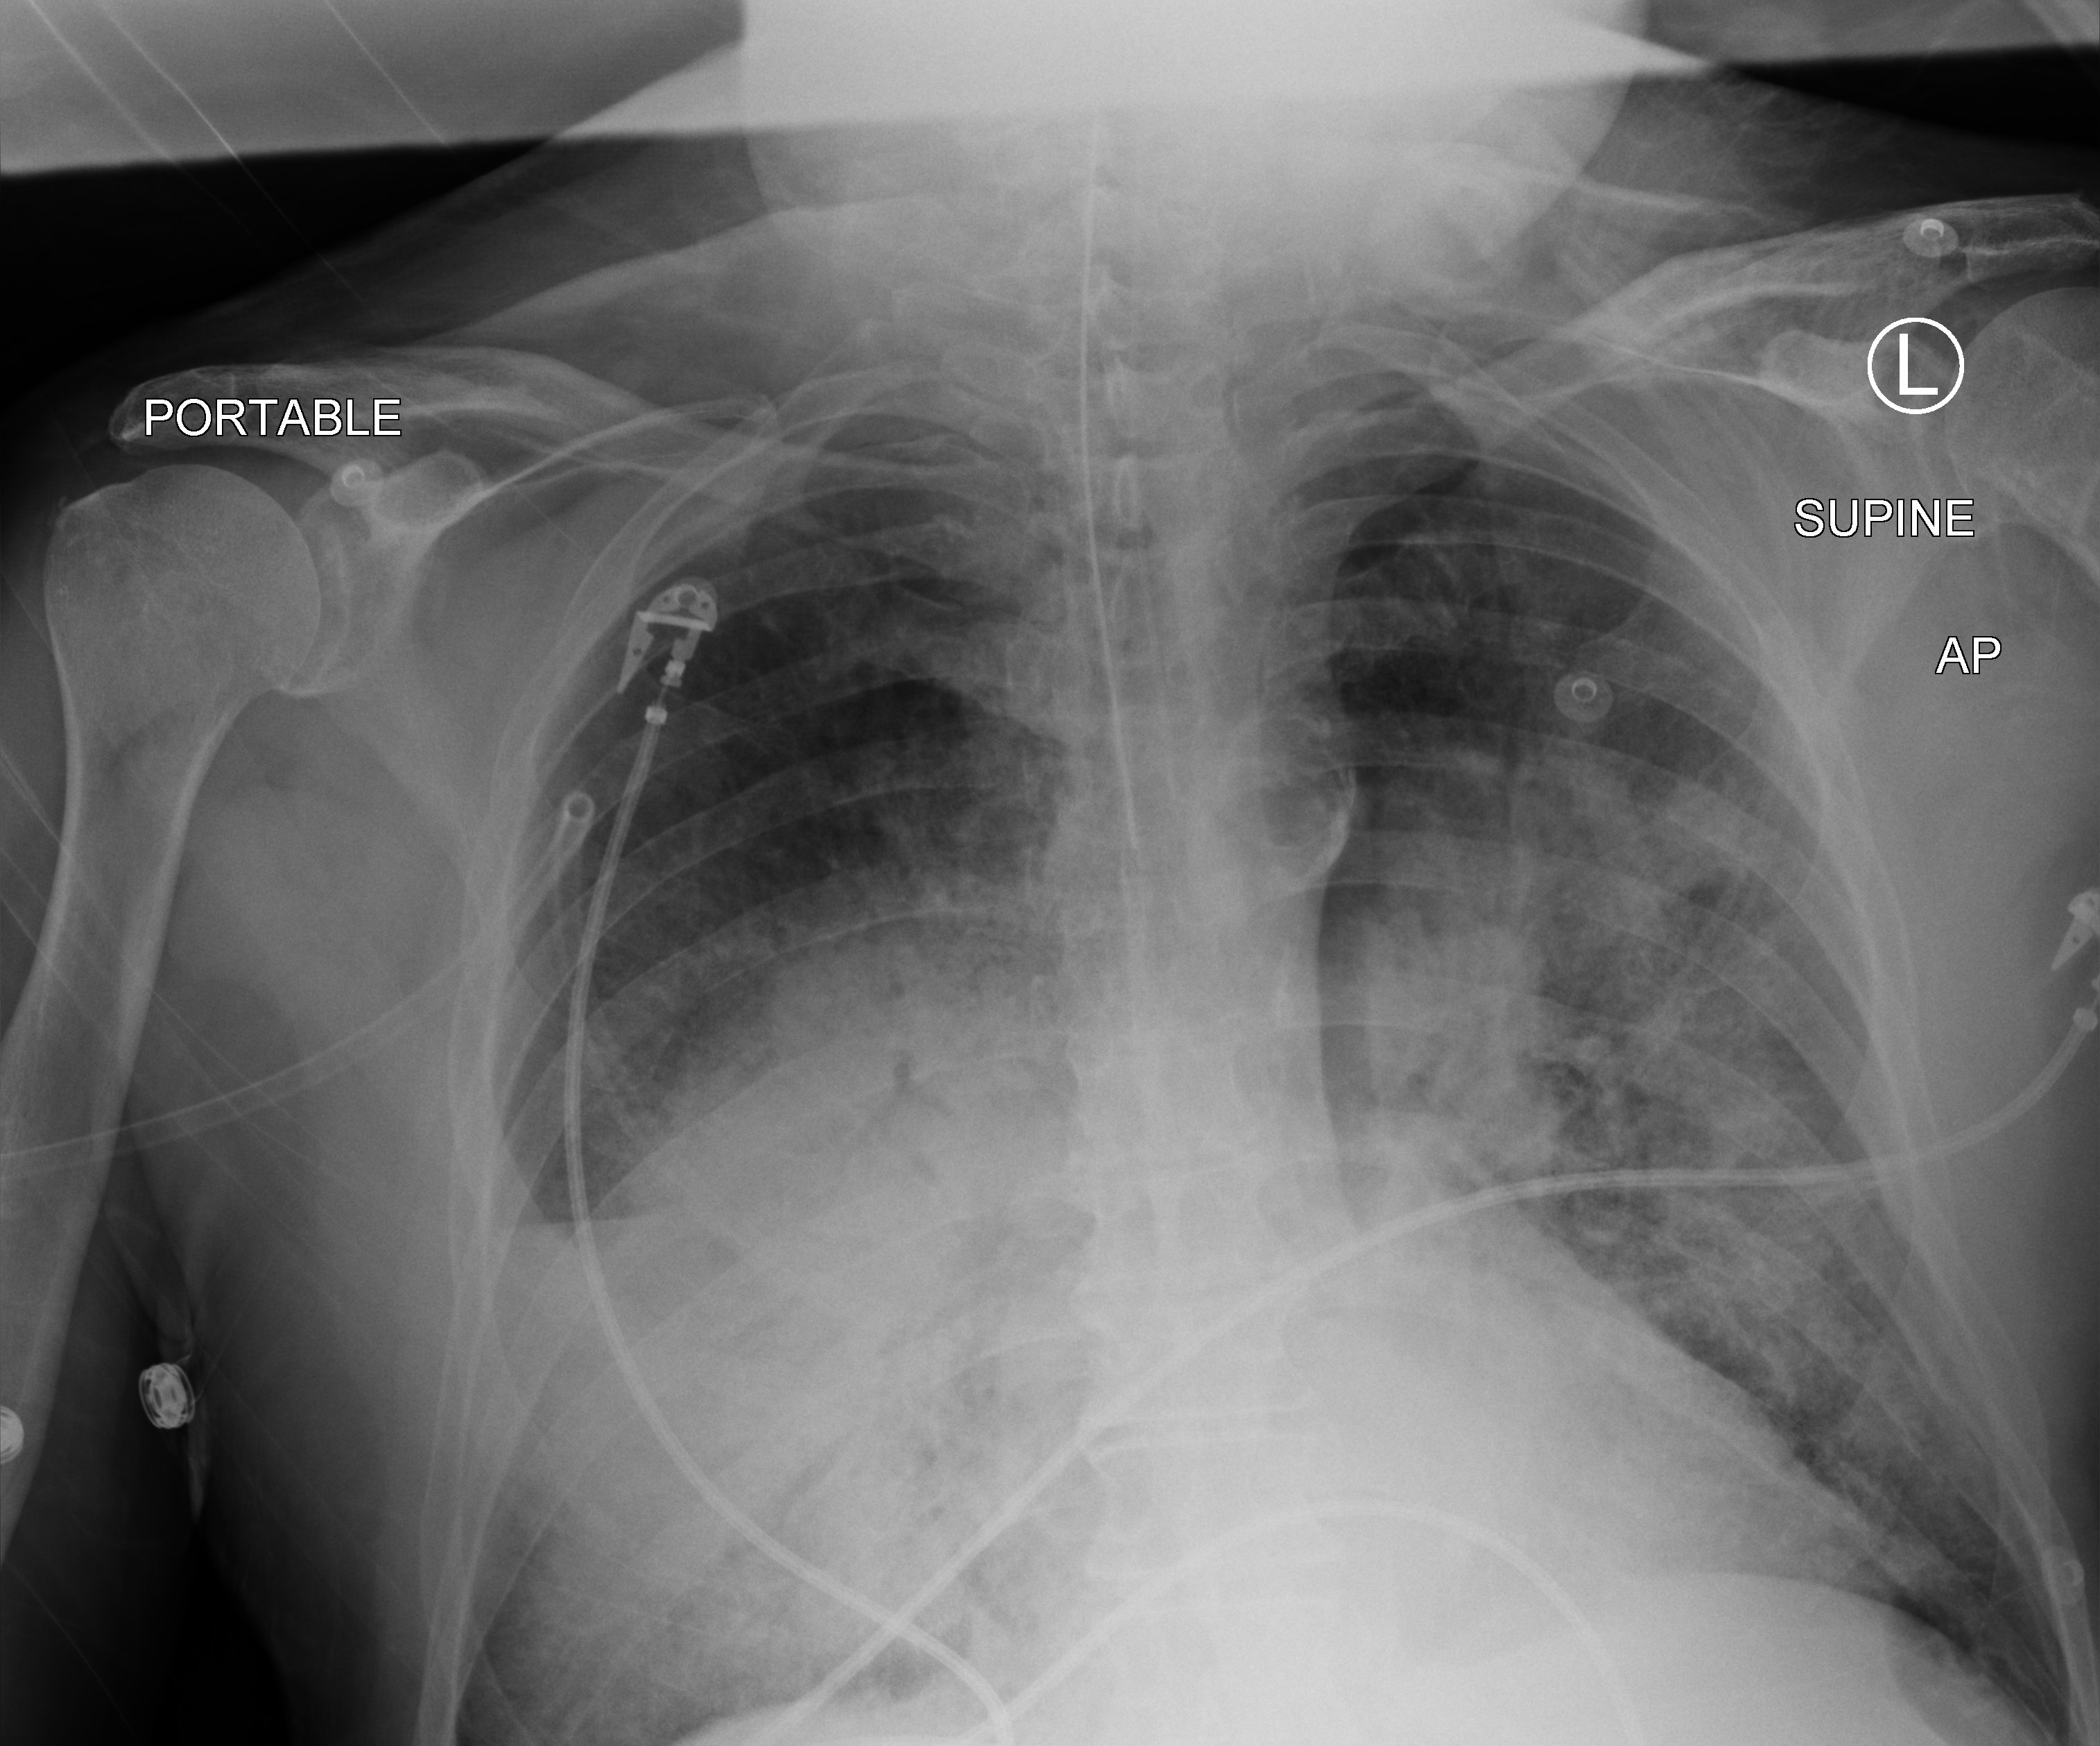
Chest X-ray (portable); anteroposterior (AP) projection. Patient hospitalised with COVID-19; male, aged 60–74 years.
Hospital-stay facts (about this admission, not read from this image; timing relative to this image not recorded): length of hospital stay: 6 days; mechanically ventilated during this hospital stay: yes; admitted to intensive care during this hospital stay: yes.